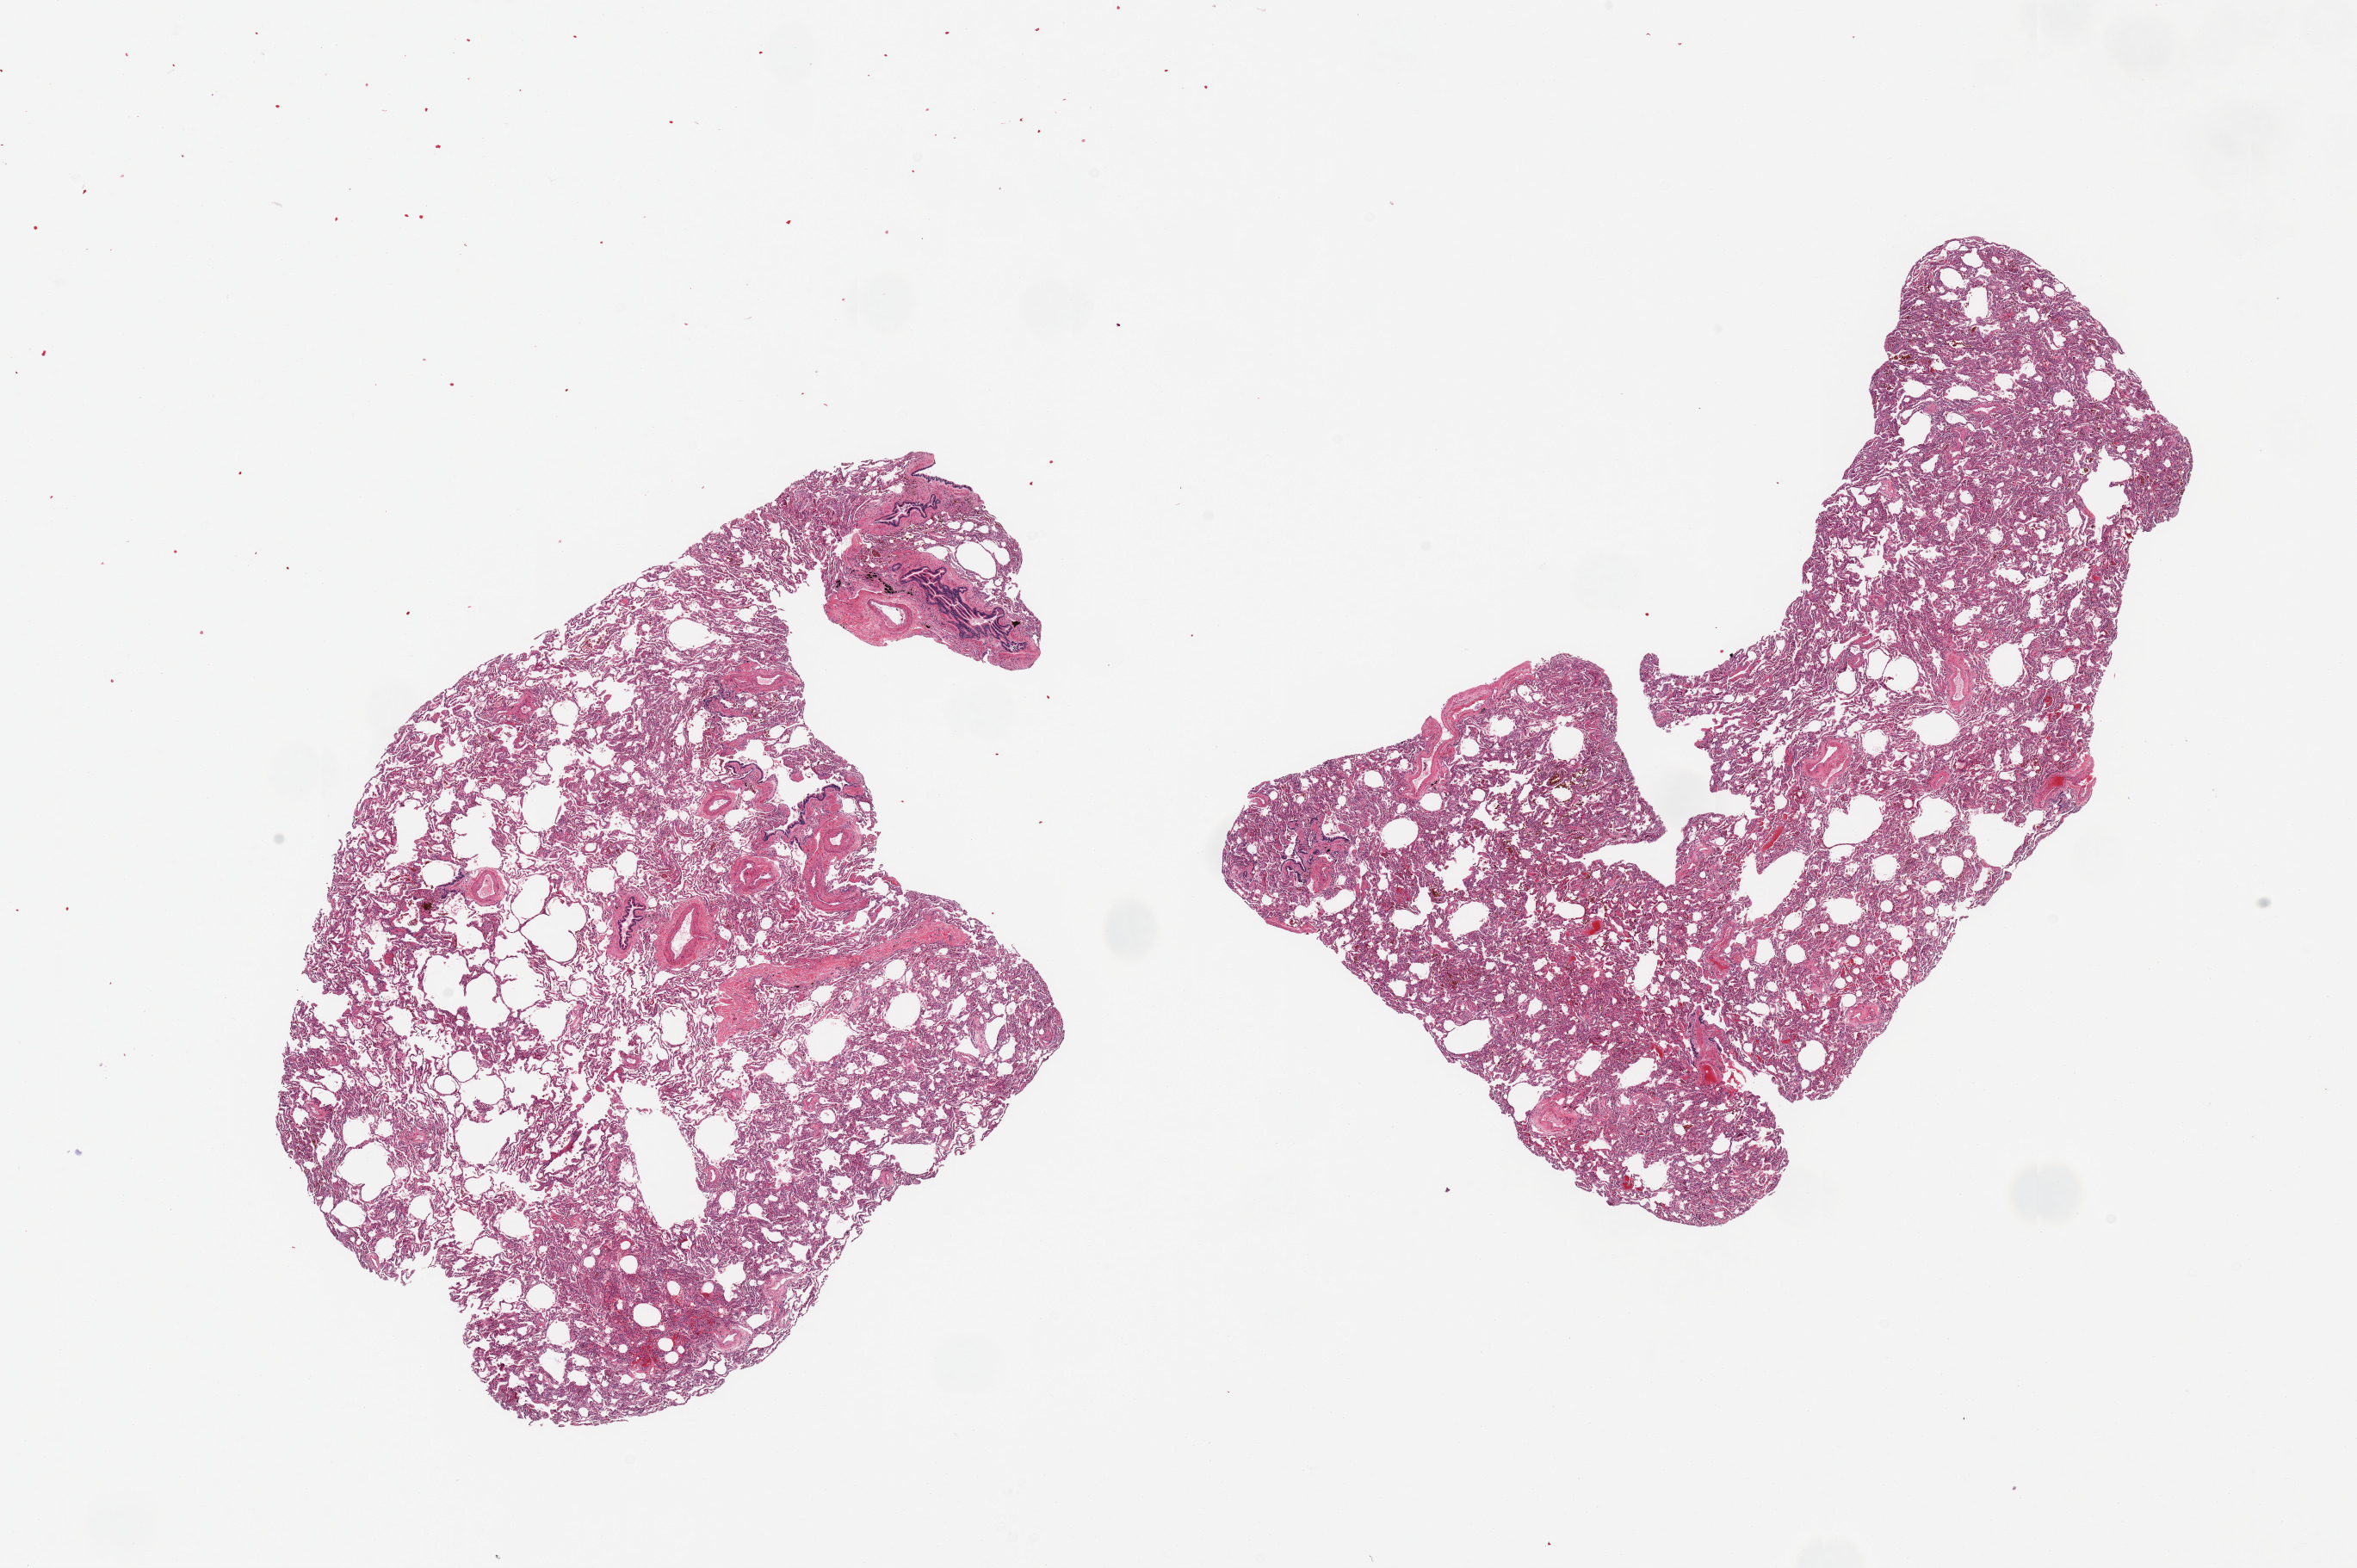
Digitized haematoxylin and eosin-stained section, whole scanned area (about 21.7 x 14.4 mm, acquisition: 20x scan) shown as a low-resolution overview. PAXgene-fixed, paraffin-embedded tissue. Target tissue: lung. Donor tissue sample. Male donor.
Reviewer comment on this tissue sample: 2 pieces; foci of mild emphysema, no fibrosis.